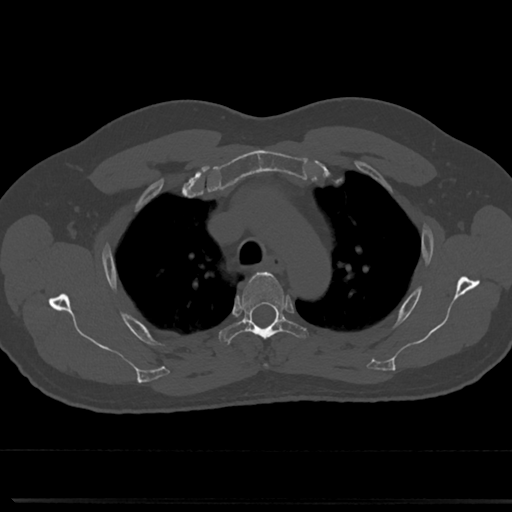
CT including the spine, one axial slice. Slice 555 of 817 in the series (ordered by position). 120 kVp. Bone window (W 1800 / L 400 HU). 0.5 mm slice thickness. 512 × 512 image matrix, field of view 355 × 355 mm. Patient: male, 61 years. From the clinical record (not read from this slice): primary cancer: prostate.
Structures marked on this image (semi-automatic segmentation, software-assisted and operator-edited):
- T3 vertebra: bounding box (x1, y1, x2, y2) in pixels: (264, 363, 269, 368)
- T4 vertebra: (219, 272, 309, 343)